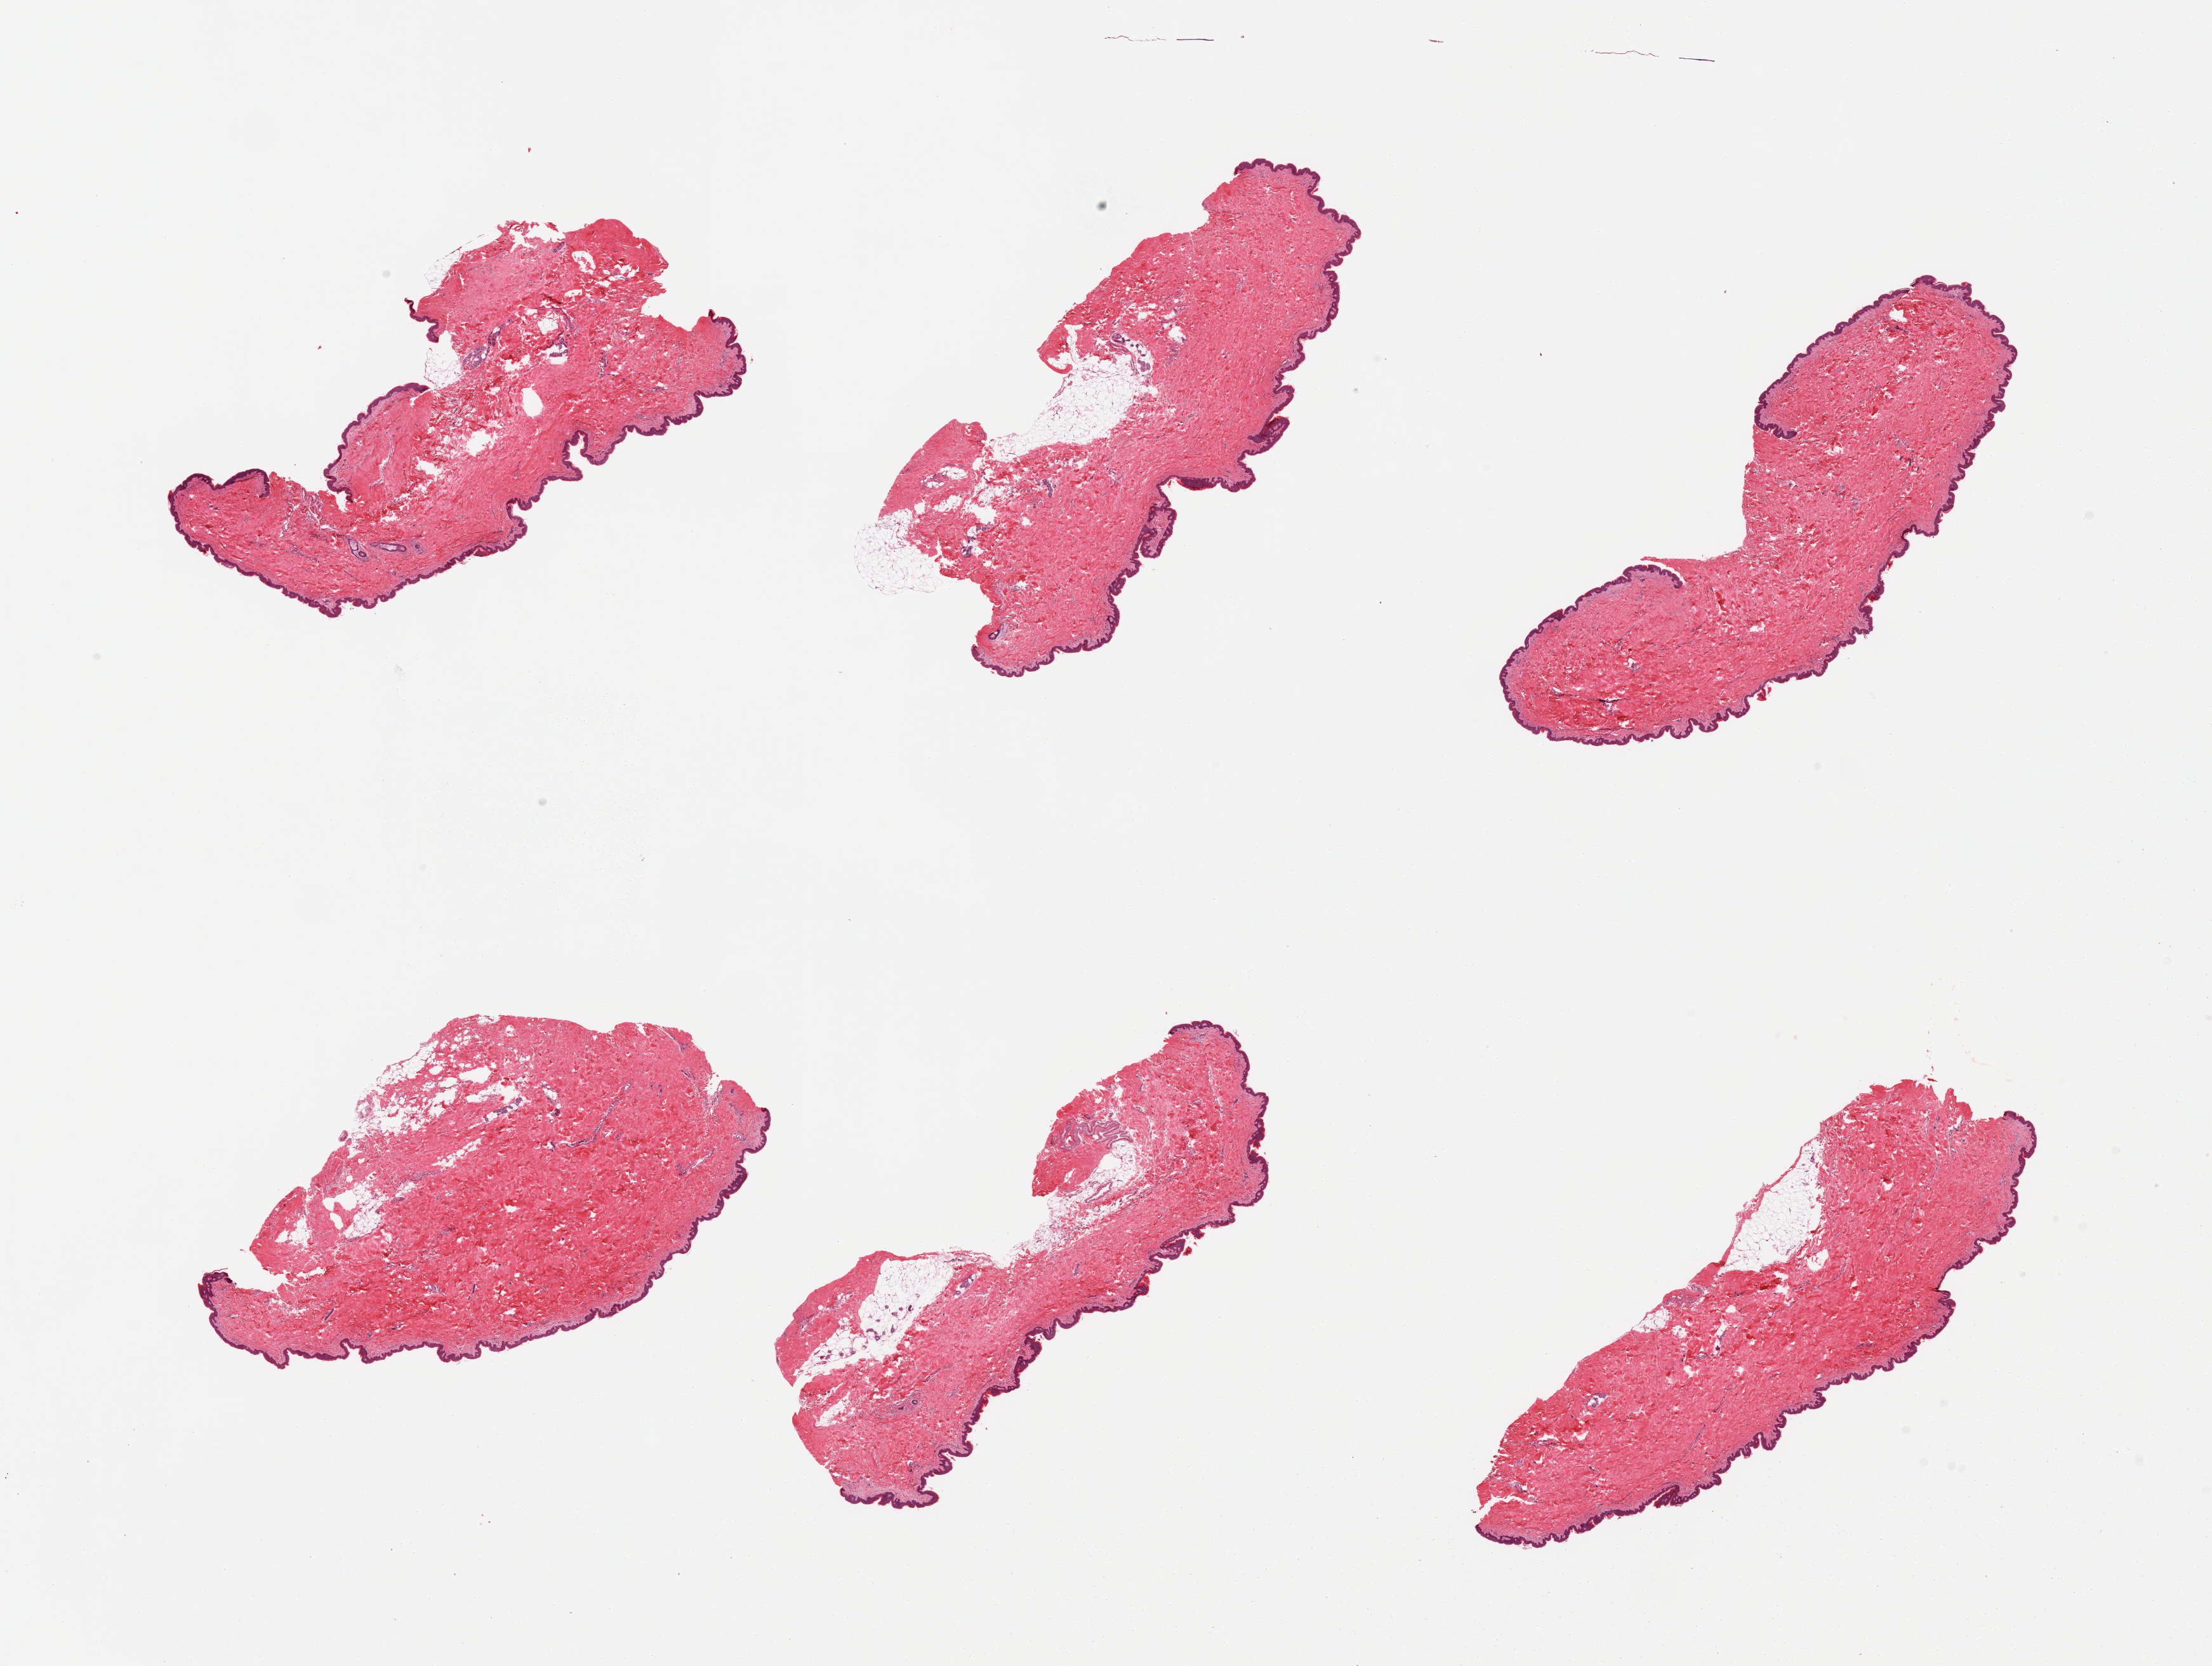
Digitized hematoxylin and eosin (H&E)-stained section, brightfield, whole scanned area (about 27.6 x 20.8 mm) shown as a low-resolution overview. PAXgene-fixed, paraffin-embedded tissue. Target tissue: skin of suprapubic region. Donor tissue sample.
Reviewer comment on this tissue sample: 6 pieces, minimal dermal fat.